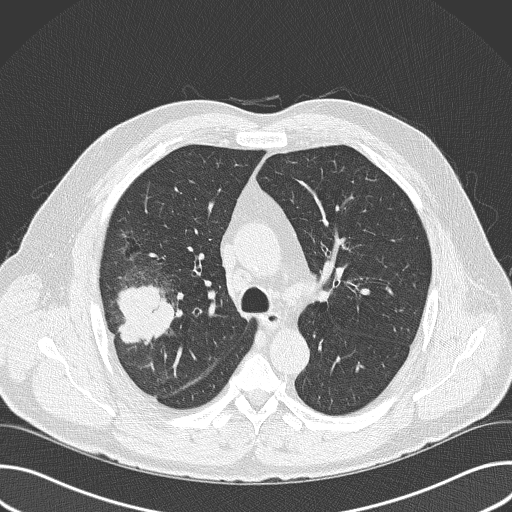
Chest CT (low-dose screening protocol), one axial image. Baseline screening round. Lung window (W 1500 / L -600 HU). Male participant, aged 56 years at enrolment. Current smoker at enrolment.
Expert reader's lesion annotation, box from (x=83, y=266) to (x=188, y=375) px. Screening reader's record for this exam (one nodule recorded; not confirmed to be the boxed lesion): non-calcified nodule or mass ≥4 mm, right upper lobe, 6 × 5 mm, spiculated (stellate) margins, soft tissue attenuation. Official screen result: positive, change unspecified: nodule(s) >= 4 mm or enlarging nodule(s), mass(es), or other non-specific abnormalities suspicious for lung cancer. Lung cancer was diagnosed 16 days after this screen: adenocarcinoma, NOS, right upper lobe, poorly differentiated (G3), stage IIB (AJCC 6th edition), 60 mm at pathology.